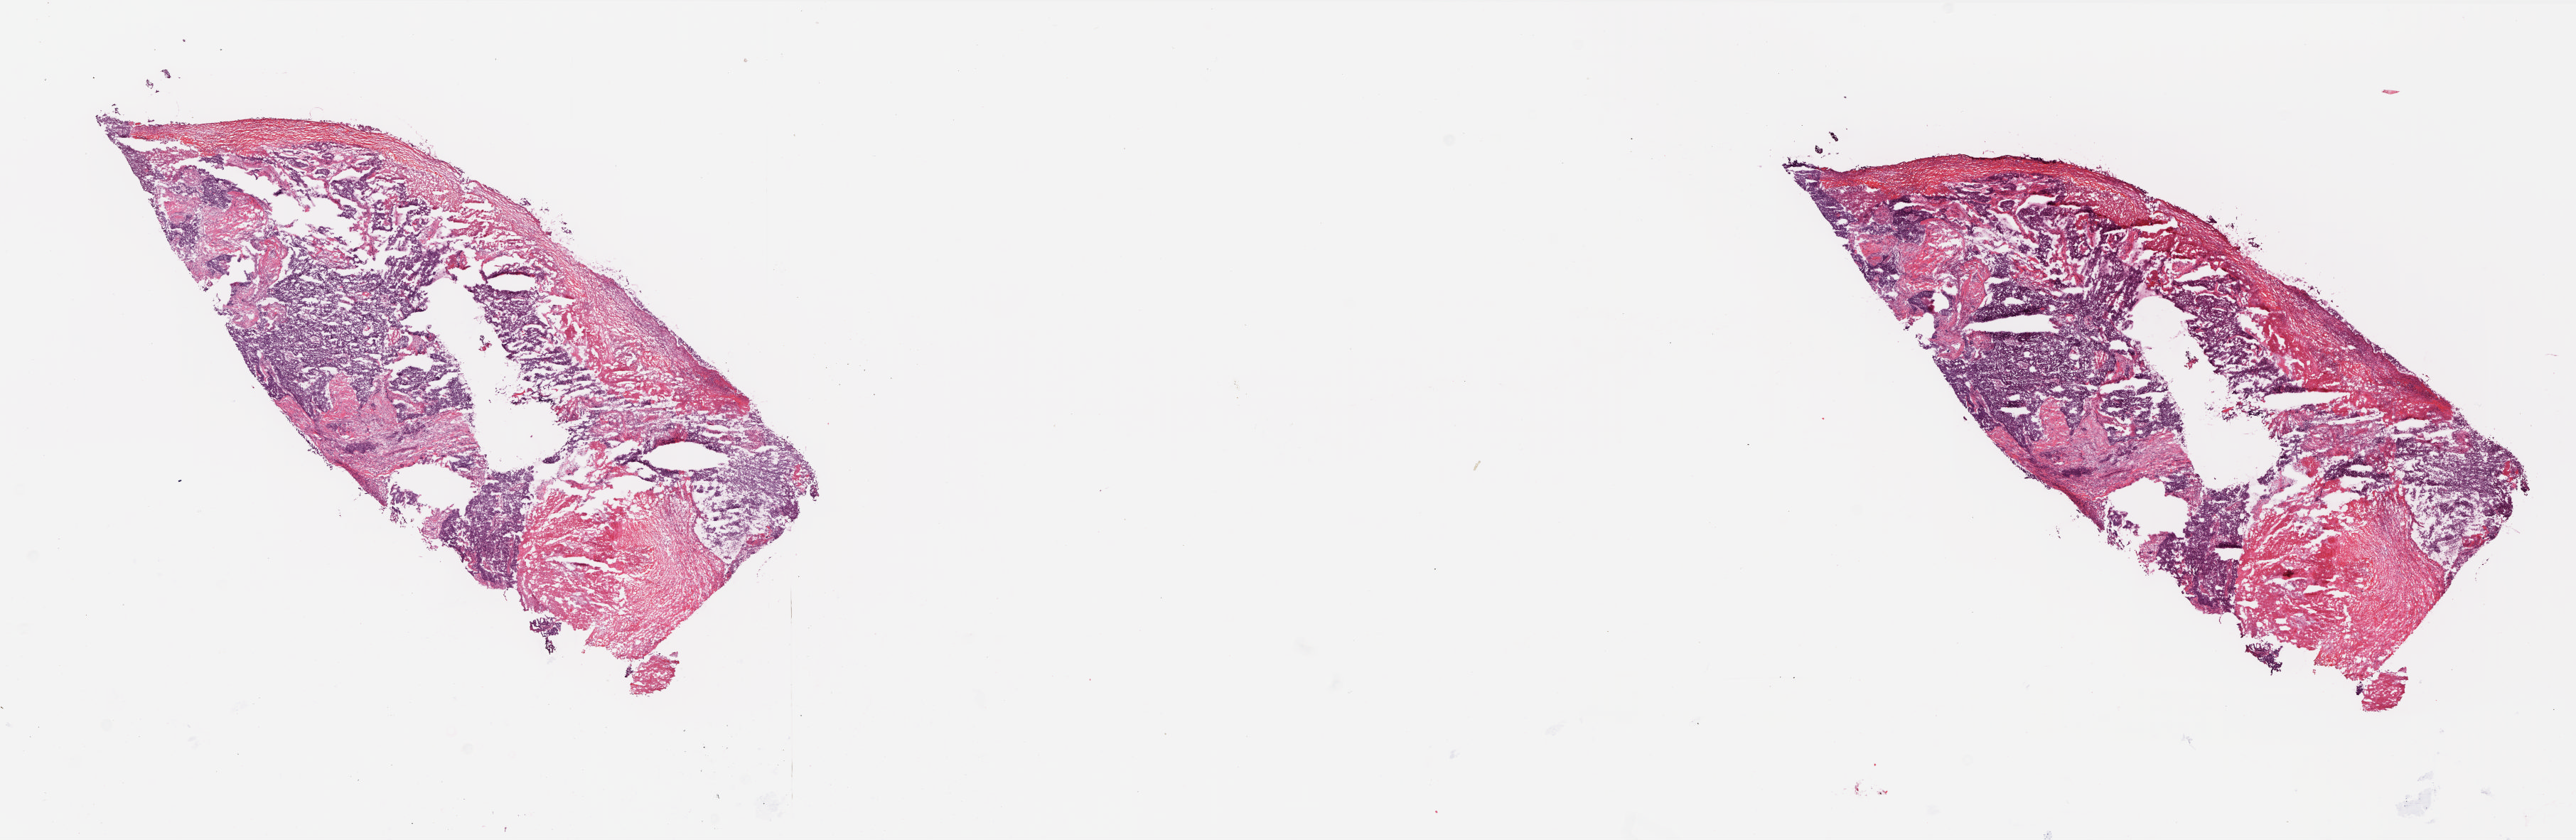
H&E whole-slide image — shown as a low-resolution overview of the whole scanned area (about 28.9 x 9.4 mm, slide scanned at 20x). Frozen section from the top of the tissue portion. Sample: primary tumour, ovary. Female, age 64 years at initial diagnosis. Composition of this section per pathologist review: tumour cells 59%, tumour nuclei 75%, normal cells 0%, stromal cells 40%, necrosis 1%.
FIGO stage: IIIC. Pathologic diagnosis: Serous cystadenocarcinoma, NOS.